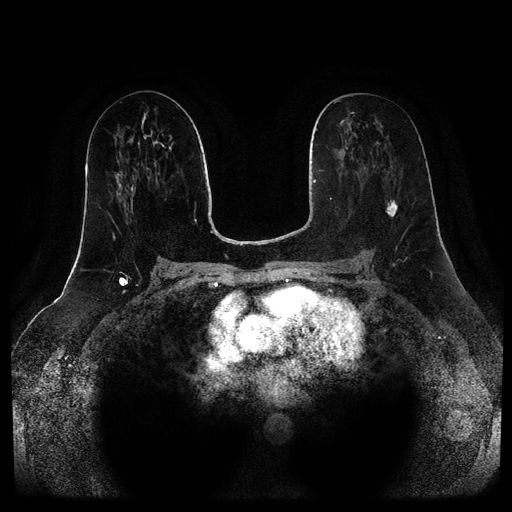
Breast MRI (dynamic contrast-enhanced, multi-phase), one axial slice. Slice 42 of 116 in the series (ordered by position). Dynamic contrast-enhanced series, time point 2 of 5 at this slice position (early post-contrast). 1.5 T. TE 2.6 ms, TR 5.2 ms. 2 mm slice thickness. 512 × 512 image matrix, field of view 380 × 380 mm. Female patient, age 57 years.
Structures marked on this image (semi-automatic segmentation, software-assisted and operator-edited):
- breast lesion (labelled 'tumour' in the annotation; benign lesions carry a separate 'benign' label): bounding box (x1, y1, x2, y2) in pixels: (386, 200, 398, 217)